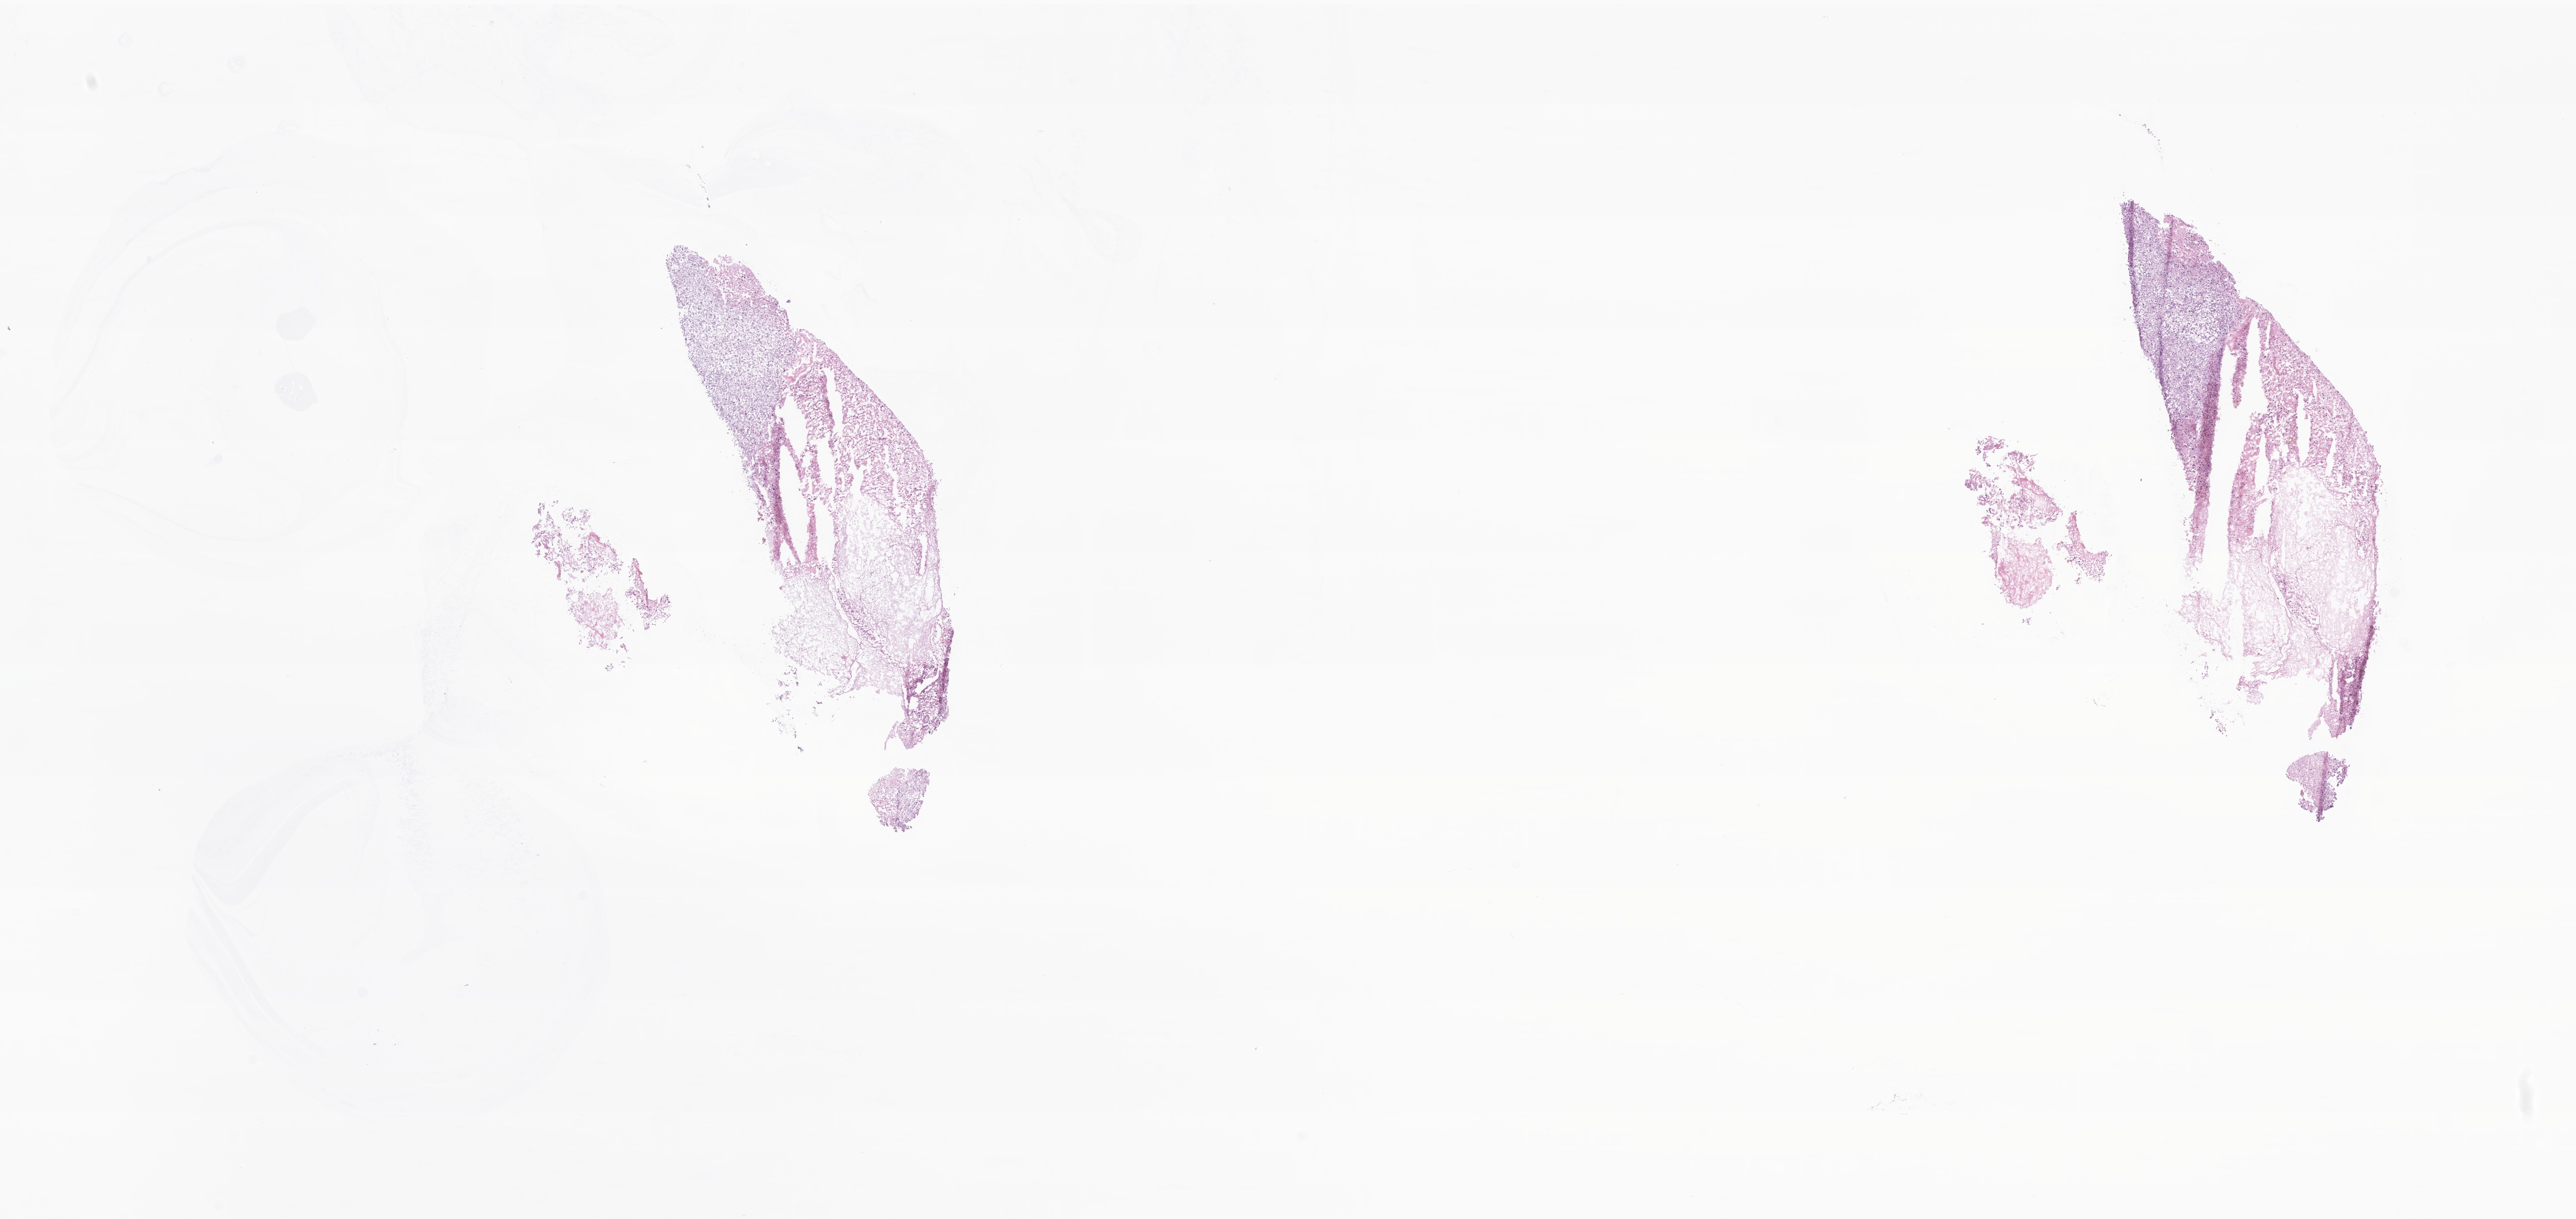
Whole-slide image, H&E stain of tumor tissue from the brain — a low-resolution overview of the entire scanned area, about 24.6 x 11.6 mm. Frozen section. Female patient, age 102 months (8 years 6 months).
Diagnosis (ICD-O-3 morphology term): Pleomorphic xanthoastrocytoma, NOS.